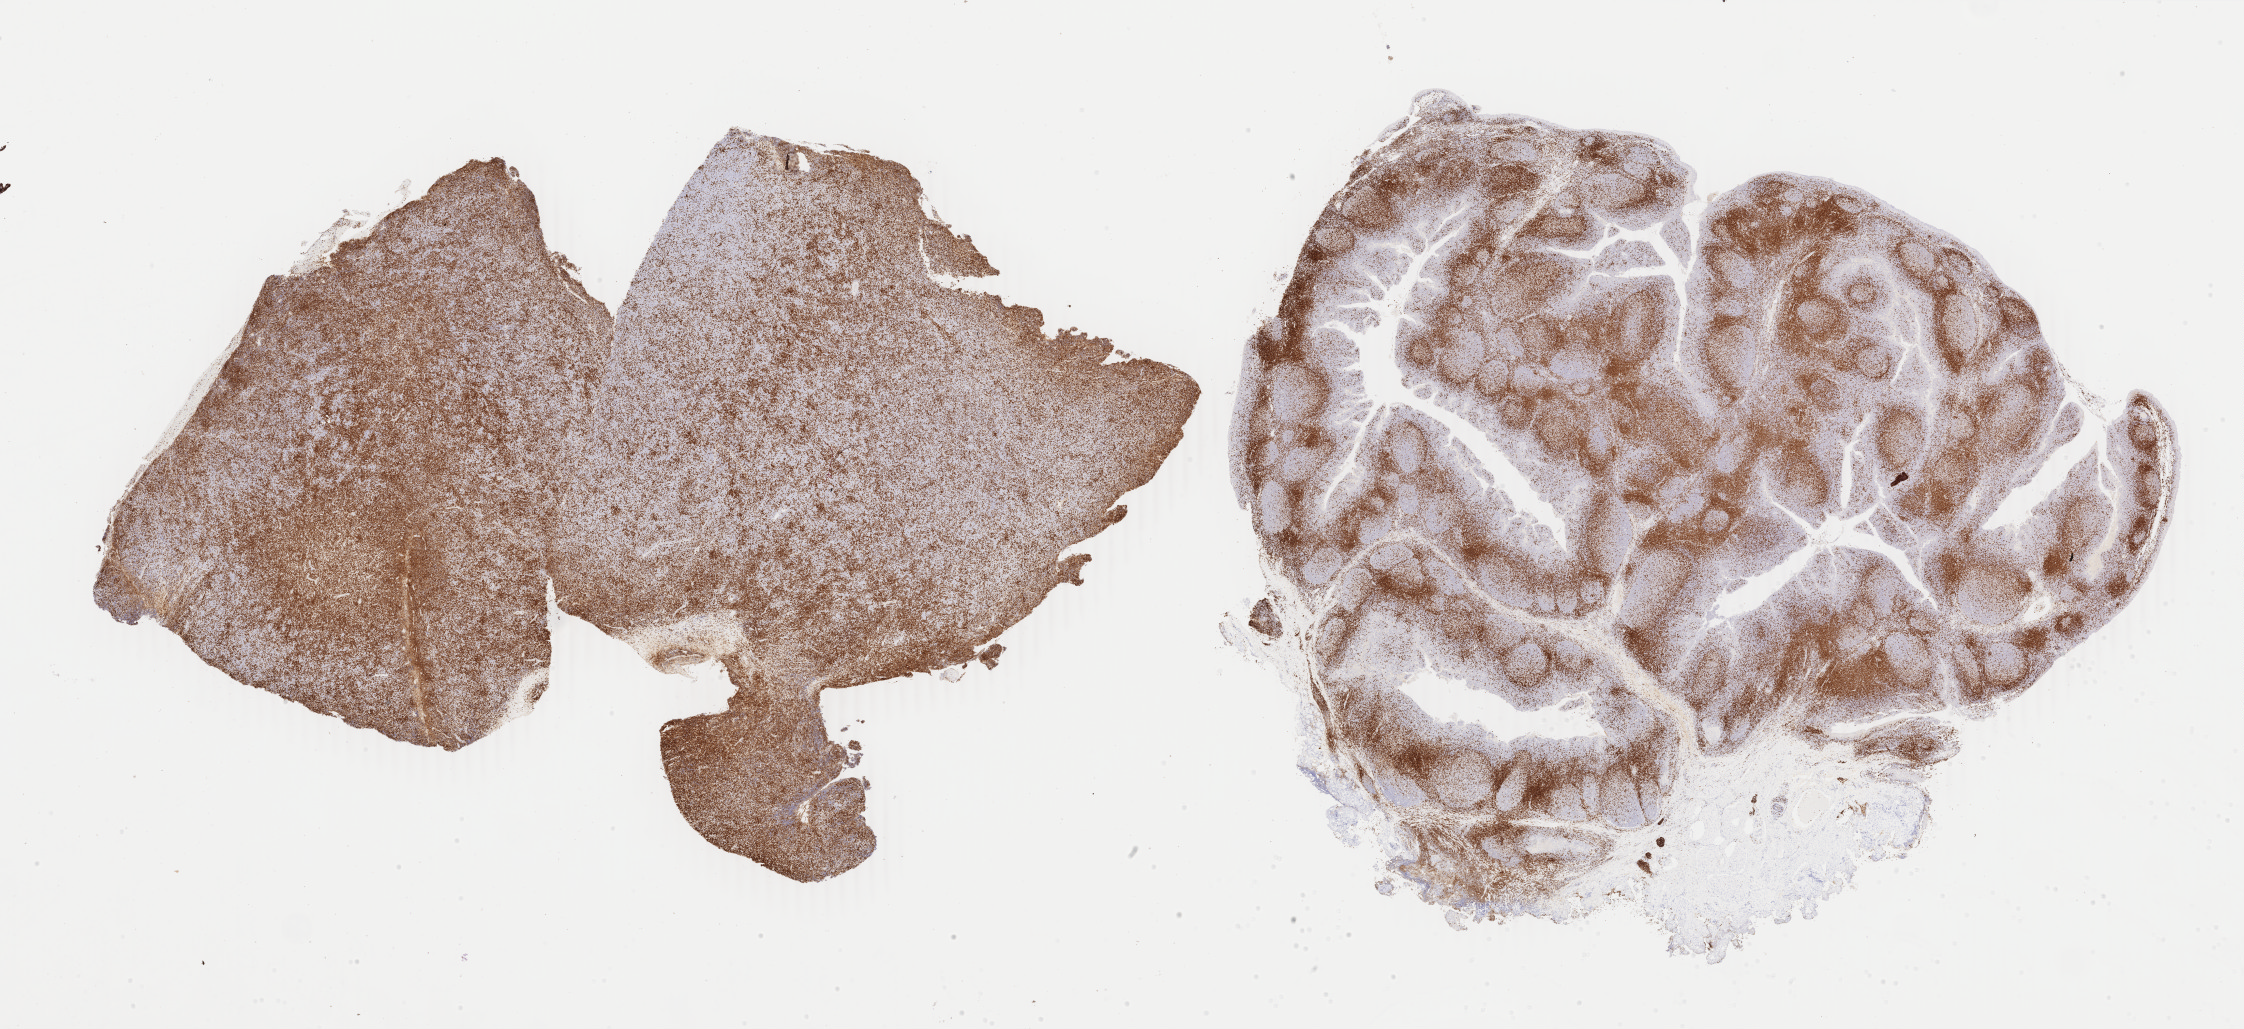
IHC for CD3, whole-slide image — shown as a low-resolution overview of the whole scanned area (about 35.7 x 16.4 mm). Tumor tissue. Male, age 7 years at initial diagnosis.
Diagnosis: Diffuse large B-cell lymphoma, NOS.